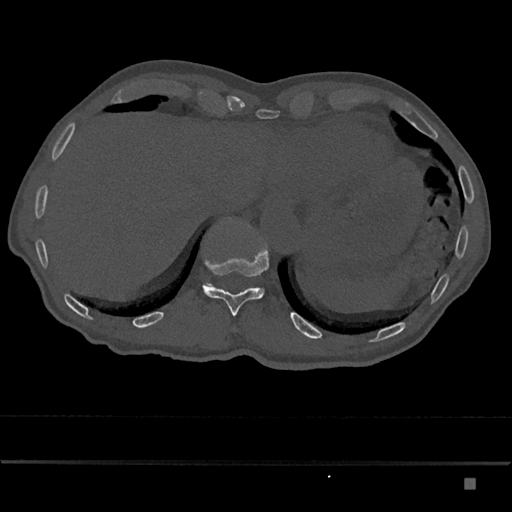
CT including the spine, one axial slice. Position 669 of 797 along the scan axis. Reconstruction kernel Br40s/3. 120 kVp. Bone window (W 1800 / L 400 HU). 0.5 mm slice thickness. 512 × 512 image matrix. Male patient, age 72 years. Case-level facts recorded for this patient, not image findings: primary cancer: prostate.
Annotated regions visible in this slice (semi-automatic segmentation, software-assisted and operator-edited):
- T11 vertebra: bounding box <202,249,269,317> (left, top, right, bottom; pixels)
- T12 vertebra: <206,217,250,286>